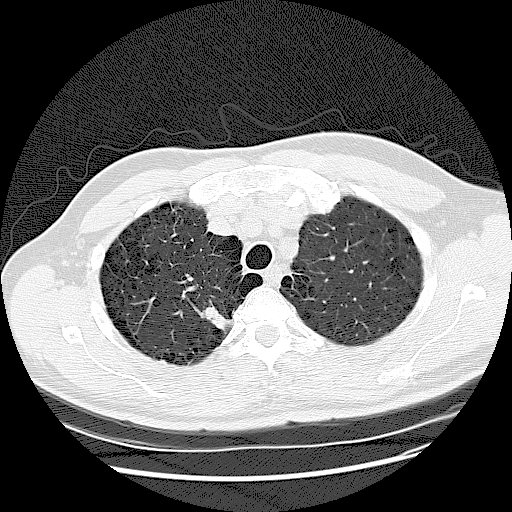
Low-dose screening chest CT, one axial slice. Position 106 of 132 along the scan axis. Reconstruction kernel LUNG. 120 kVp. Lung window (W 1500 / L -600 HU). 512 × 512 image matrix, field of view 380 × 380 mm.
Annotated regions visible in this slice (expert manual segmentation):
- lesion 1 (tumor, upper lobe of right lung): bounding box <200,301,234,334> (left, top, right, bottom; pixels)